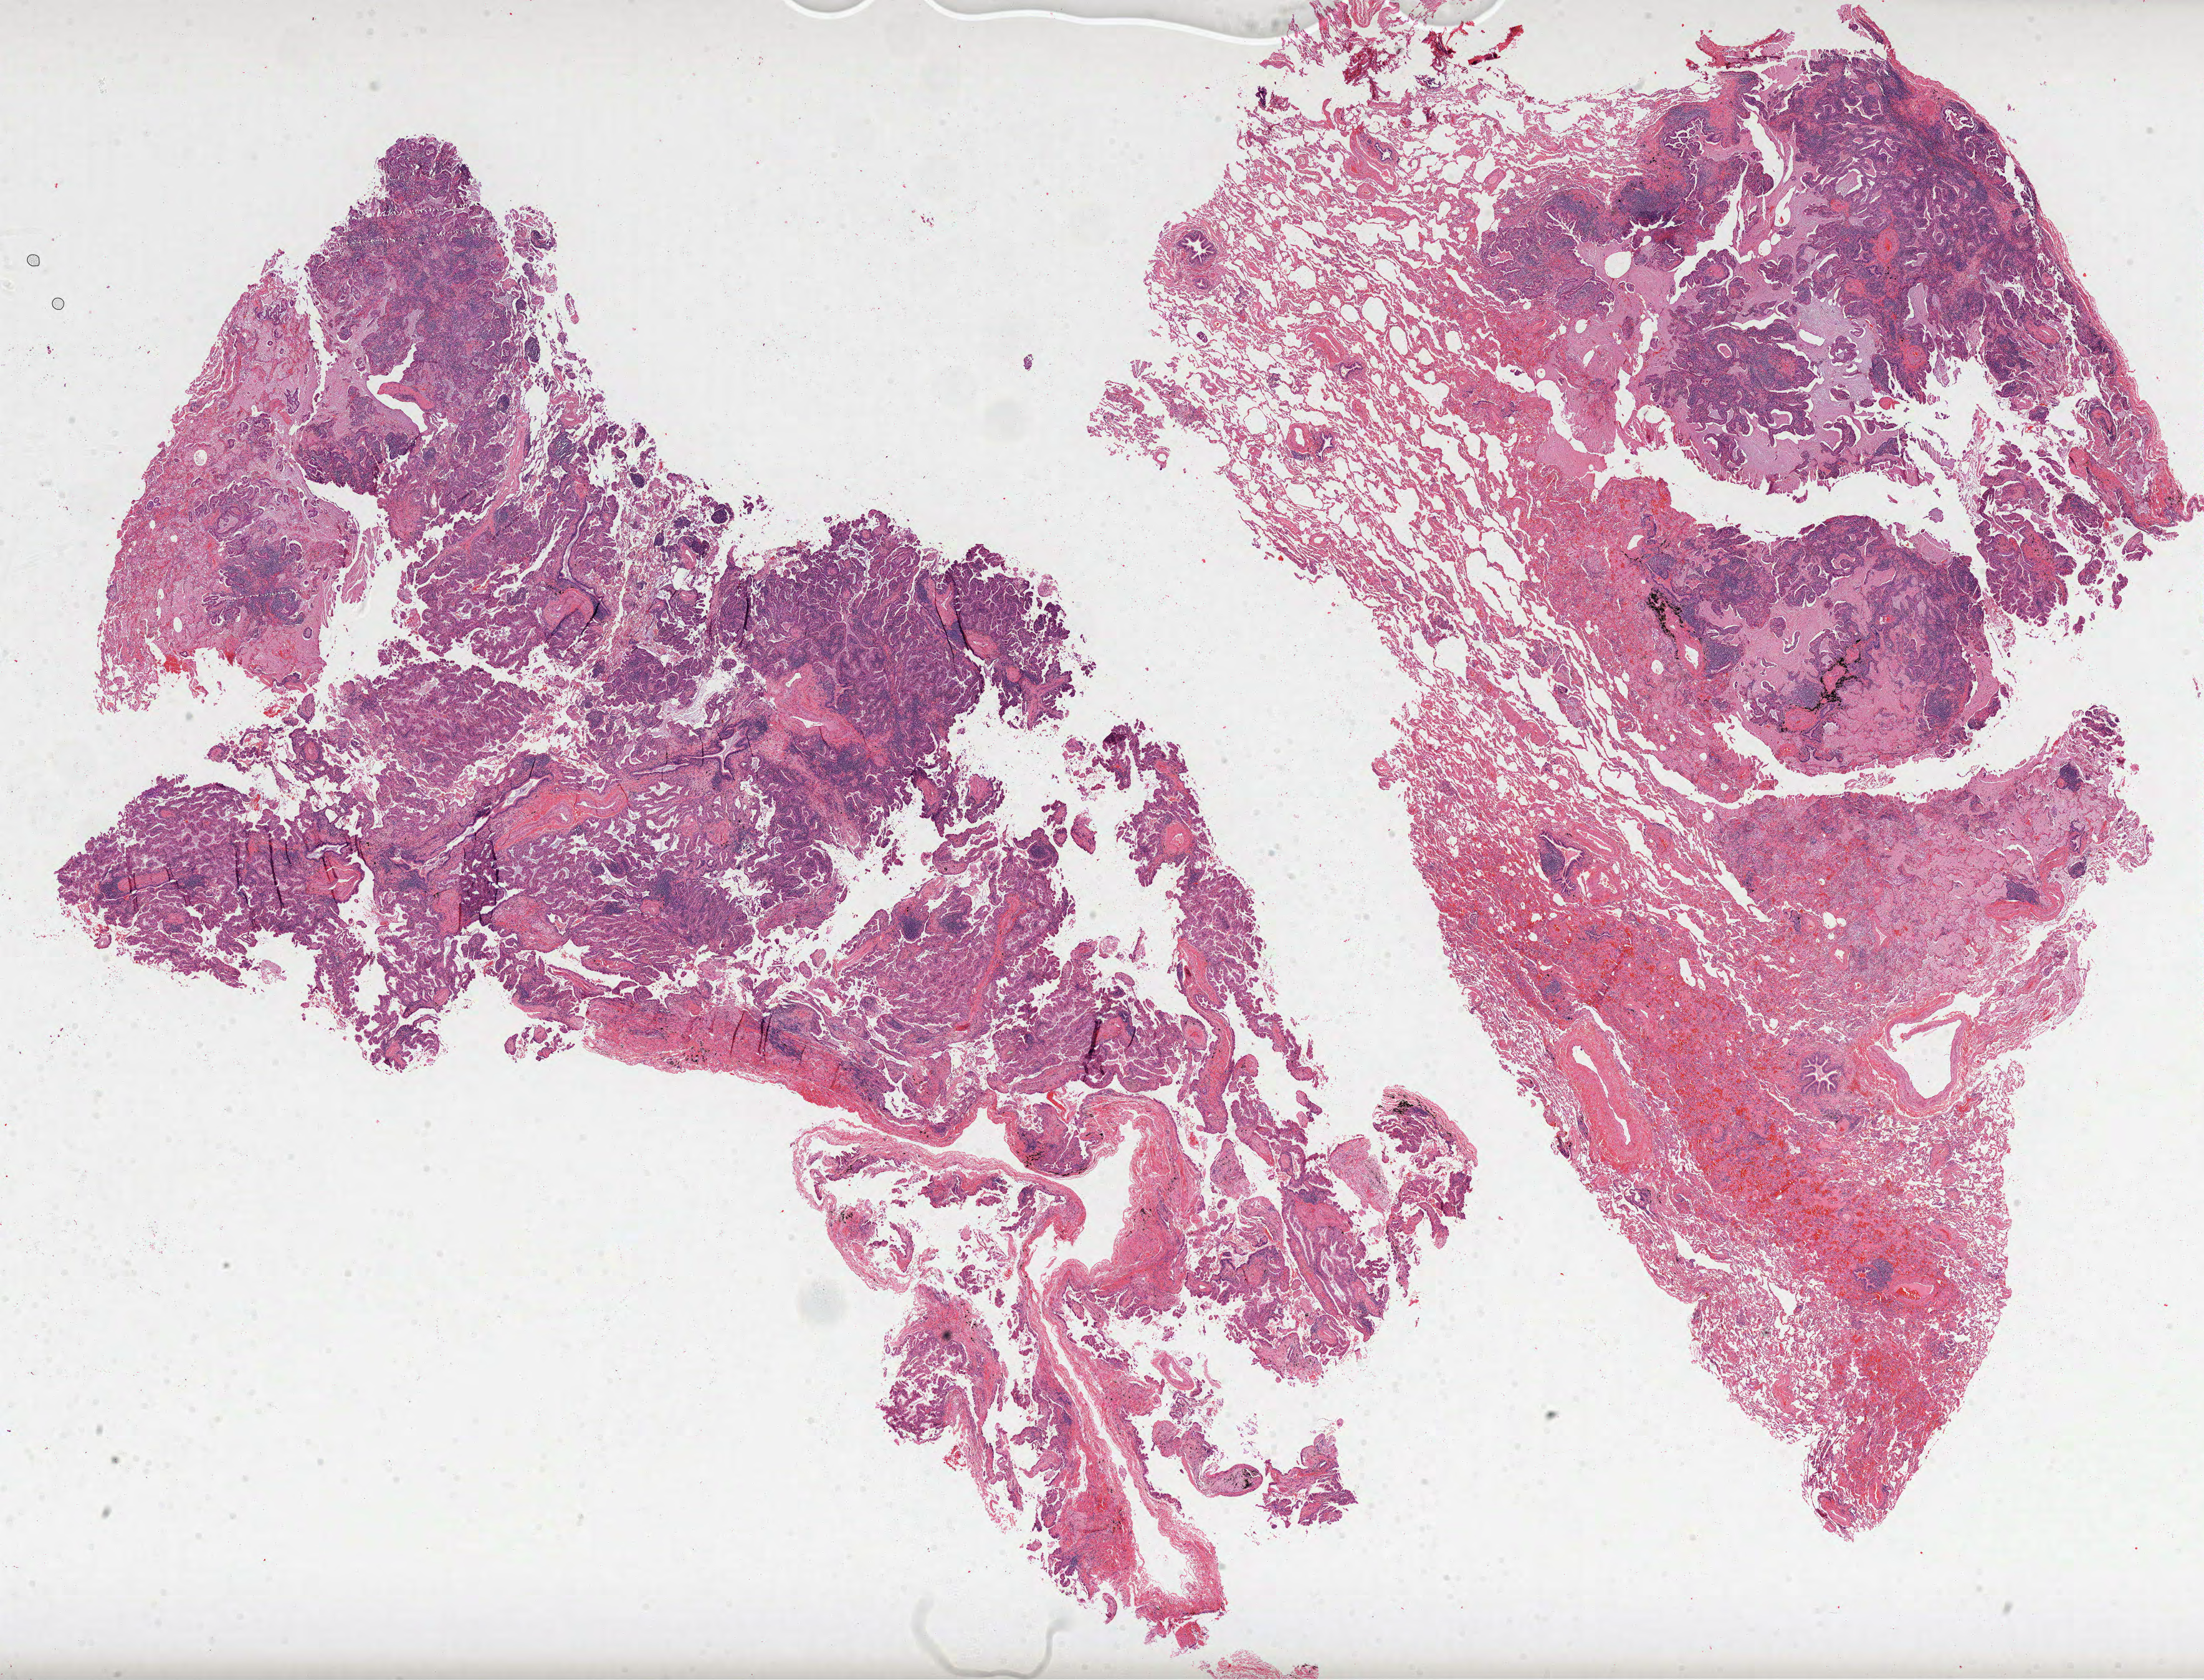
H&E whole-slide image, whole scanned area (about 28.5 x 21.7 mm) shown as a low-resolution overview, formalin-fixed paraffin-embedded (FFPE) diagnostic section, lung, primary tumour sample. Patient: male, age at initial diagnosis 85 years.
Laterality: right. Histologic diagnosis: Adenocarcinoma with mixed subtypes (lower lobe, lung).